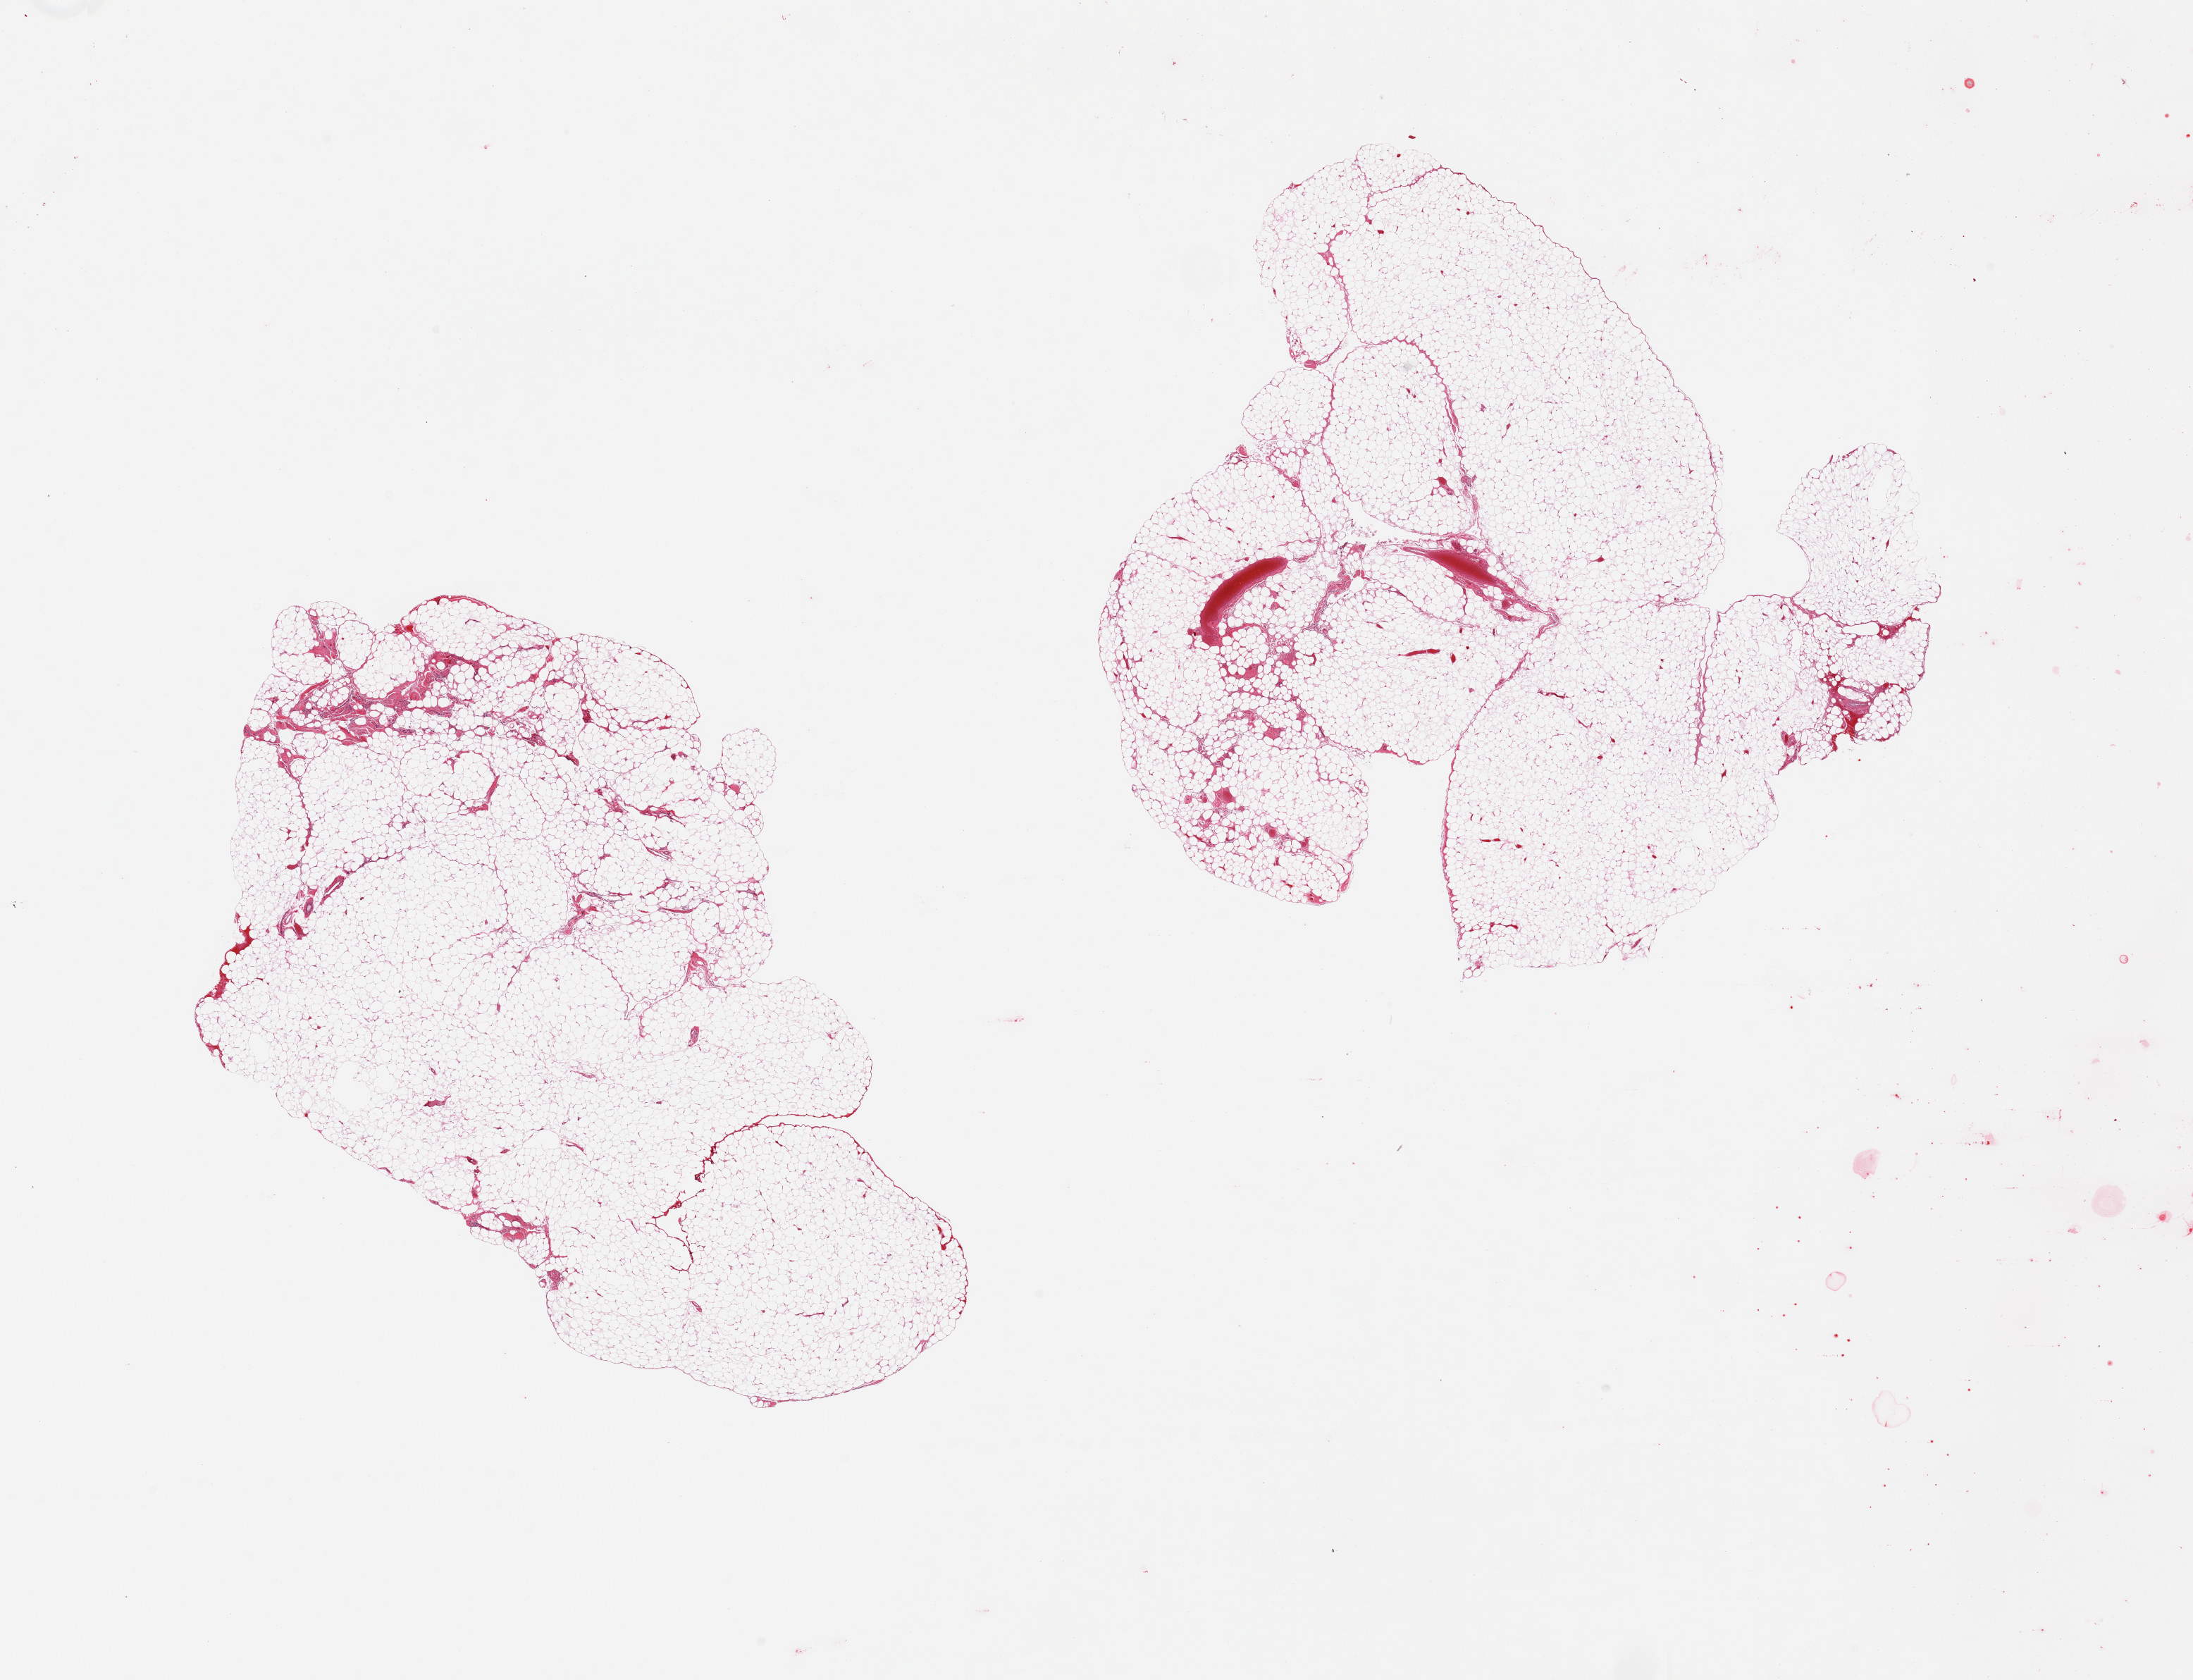
Haematoxylin and eosin whole-slide image, brightfield, whole scanned area (about 24.6 x 18.9 mm) shown as a low-resolution overview; PAXgene-fixed paraffin-embedded (PFPE) section; target tissue: omentum; donor tissue sample. Male donor.
Reviewer comment on this tissue sample: 2 pieces.